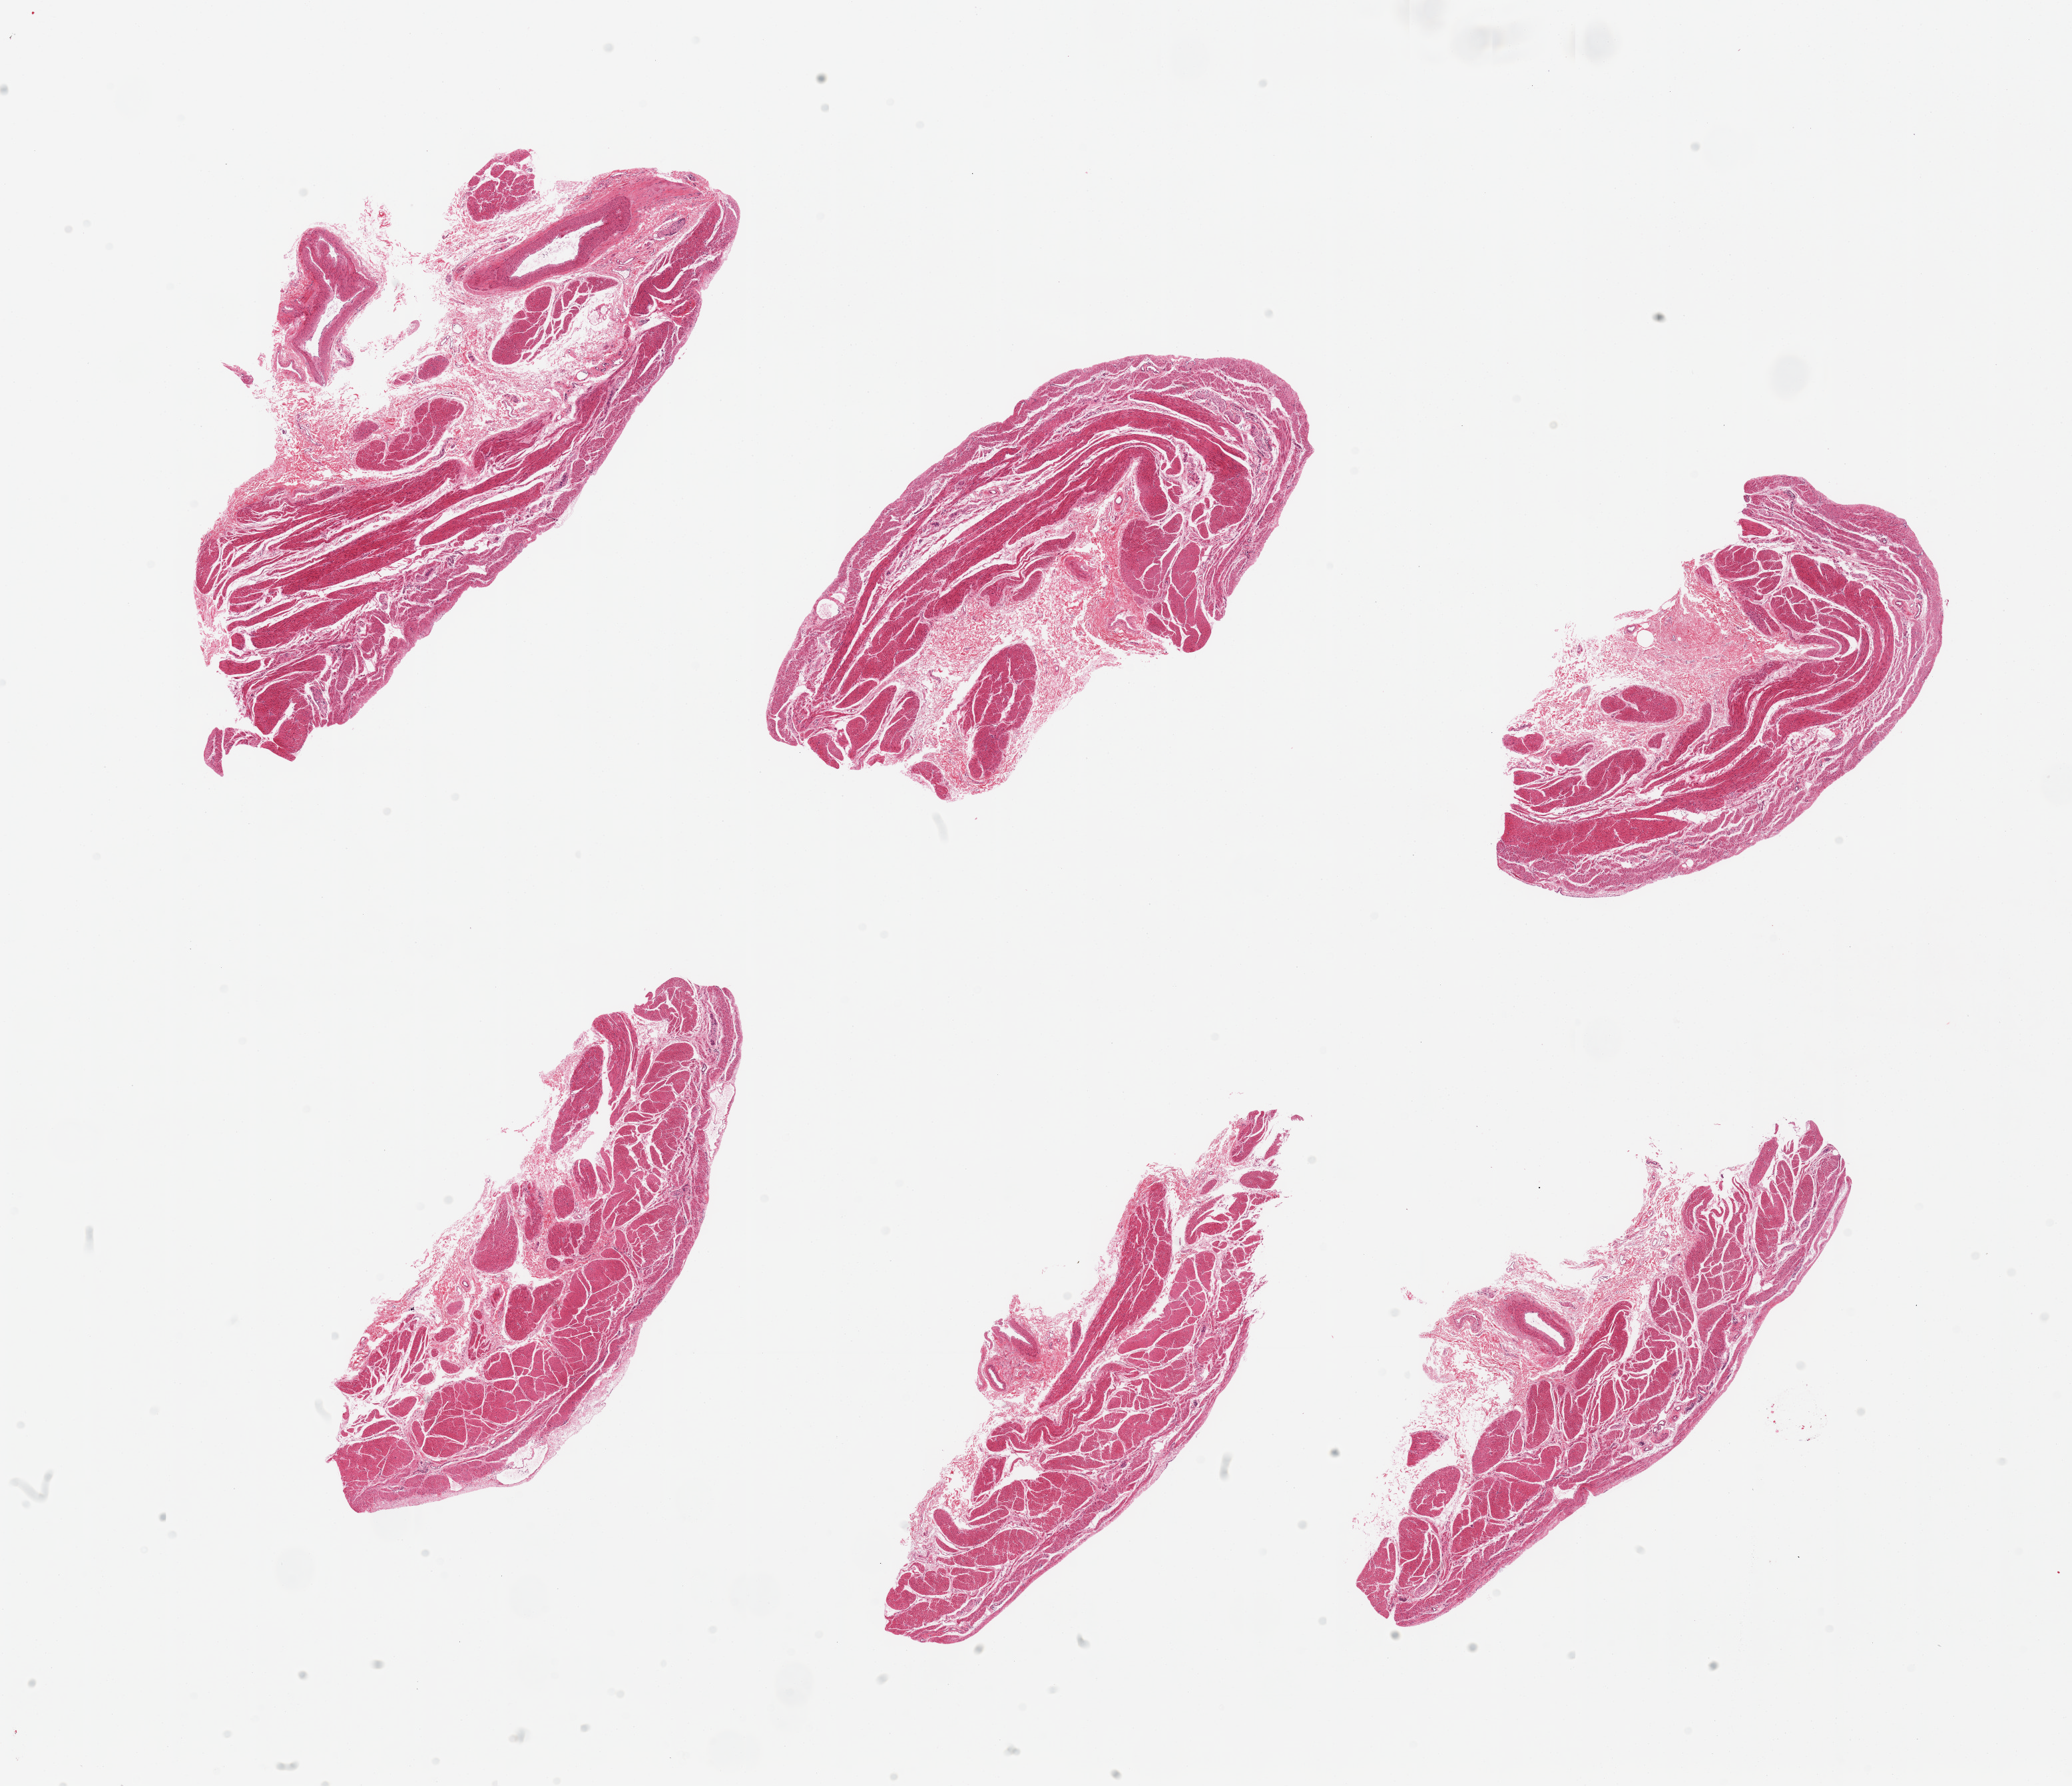
Whole-slide image, hematoxylin and eosin (H&E) stain, brightfield, a low-resolution overview of the entire scanned area, about 24.6 x 21.2 mm (acquisition: 20x scan); PAXgene-fixed, paraffin-embedded tissue; section of stomach (target tissue); tissue donor sample. Female donor.
• reviewer comment on this tissue sample: 6 pieces, muscularis only